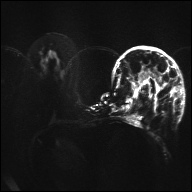
Breast MRI, one axial slice. Slice 15 of 32 in the series (ordered by position). Diffusion-weighted series; image 2 of 4 stored at this slice position (different b-values; order by instance number). 1.5 T. 4 mm slice thickness. 192 × 192 image matrix, field of view 360 × 360 mm. Female patient.
Annotated regions visible in this slice (expert manual segmentation):
- tumour on diffusion-weighted imaging: bounding box [x1, y1, x2, y2] px = [154, 67, 161, 80]